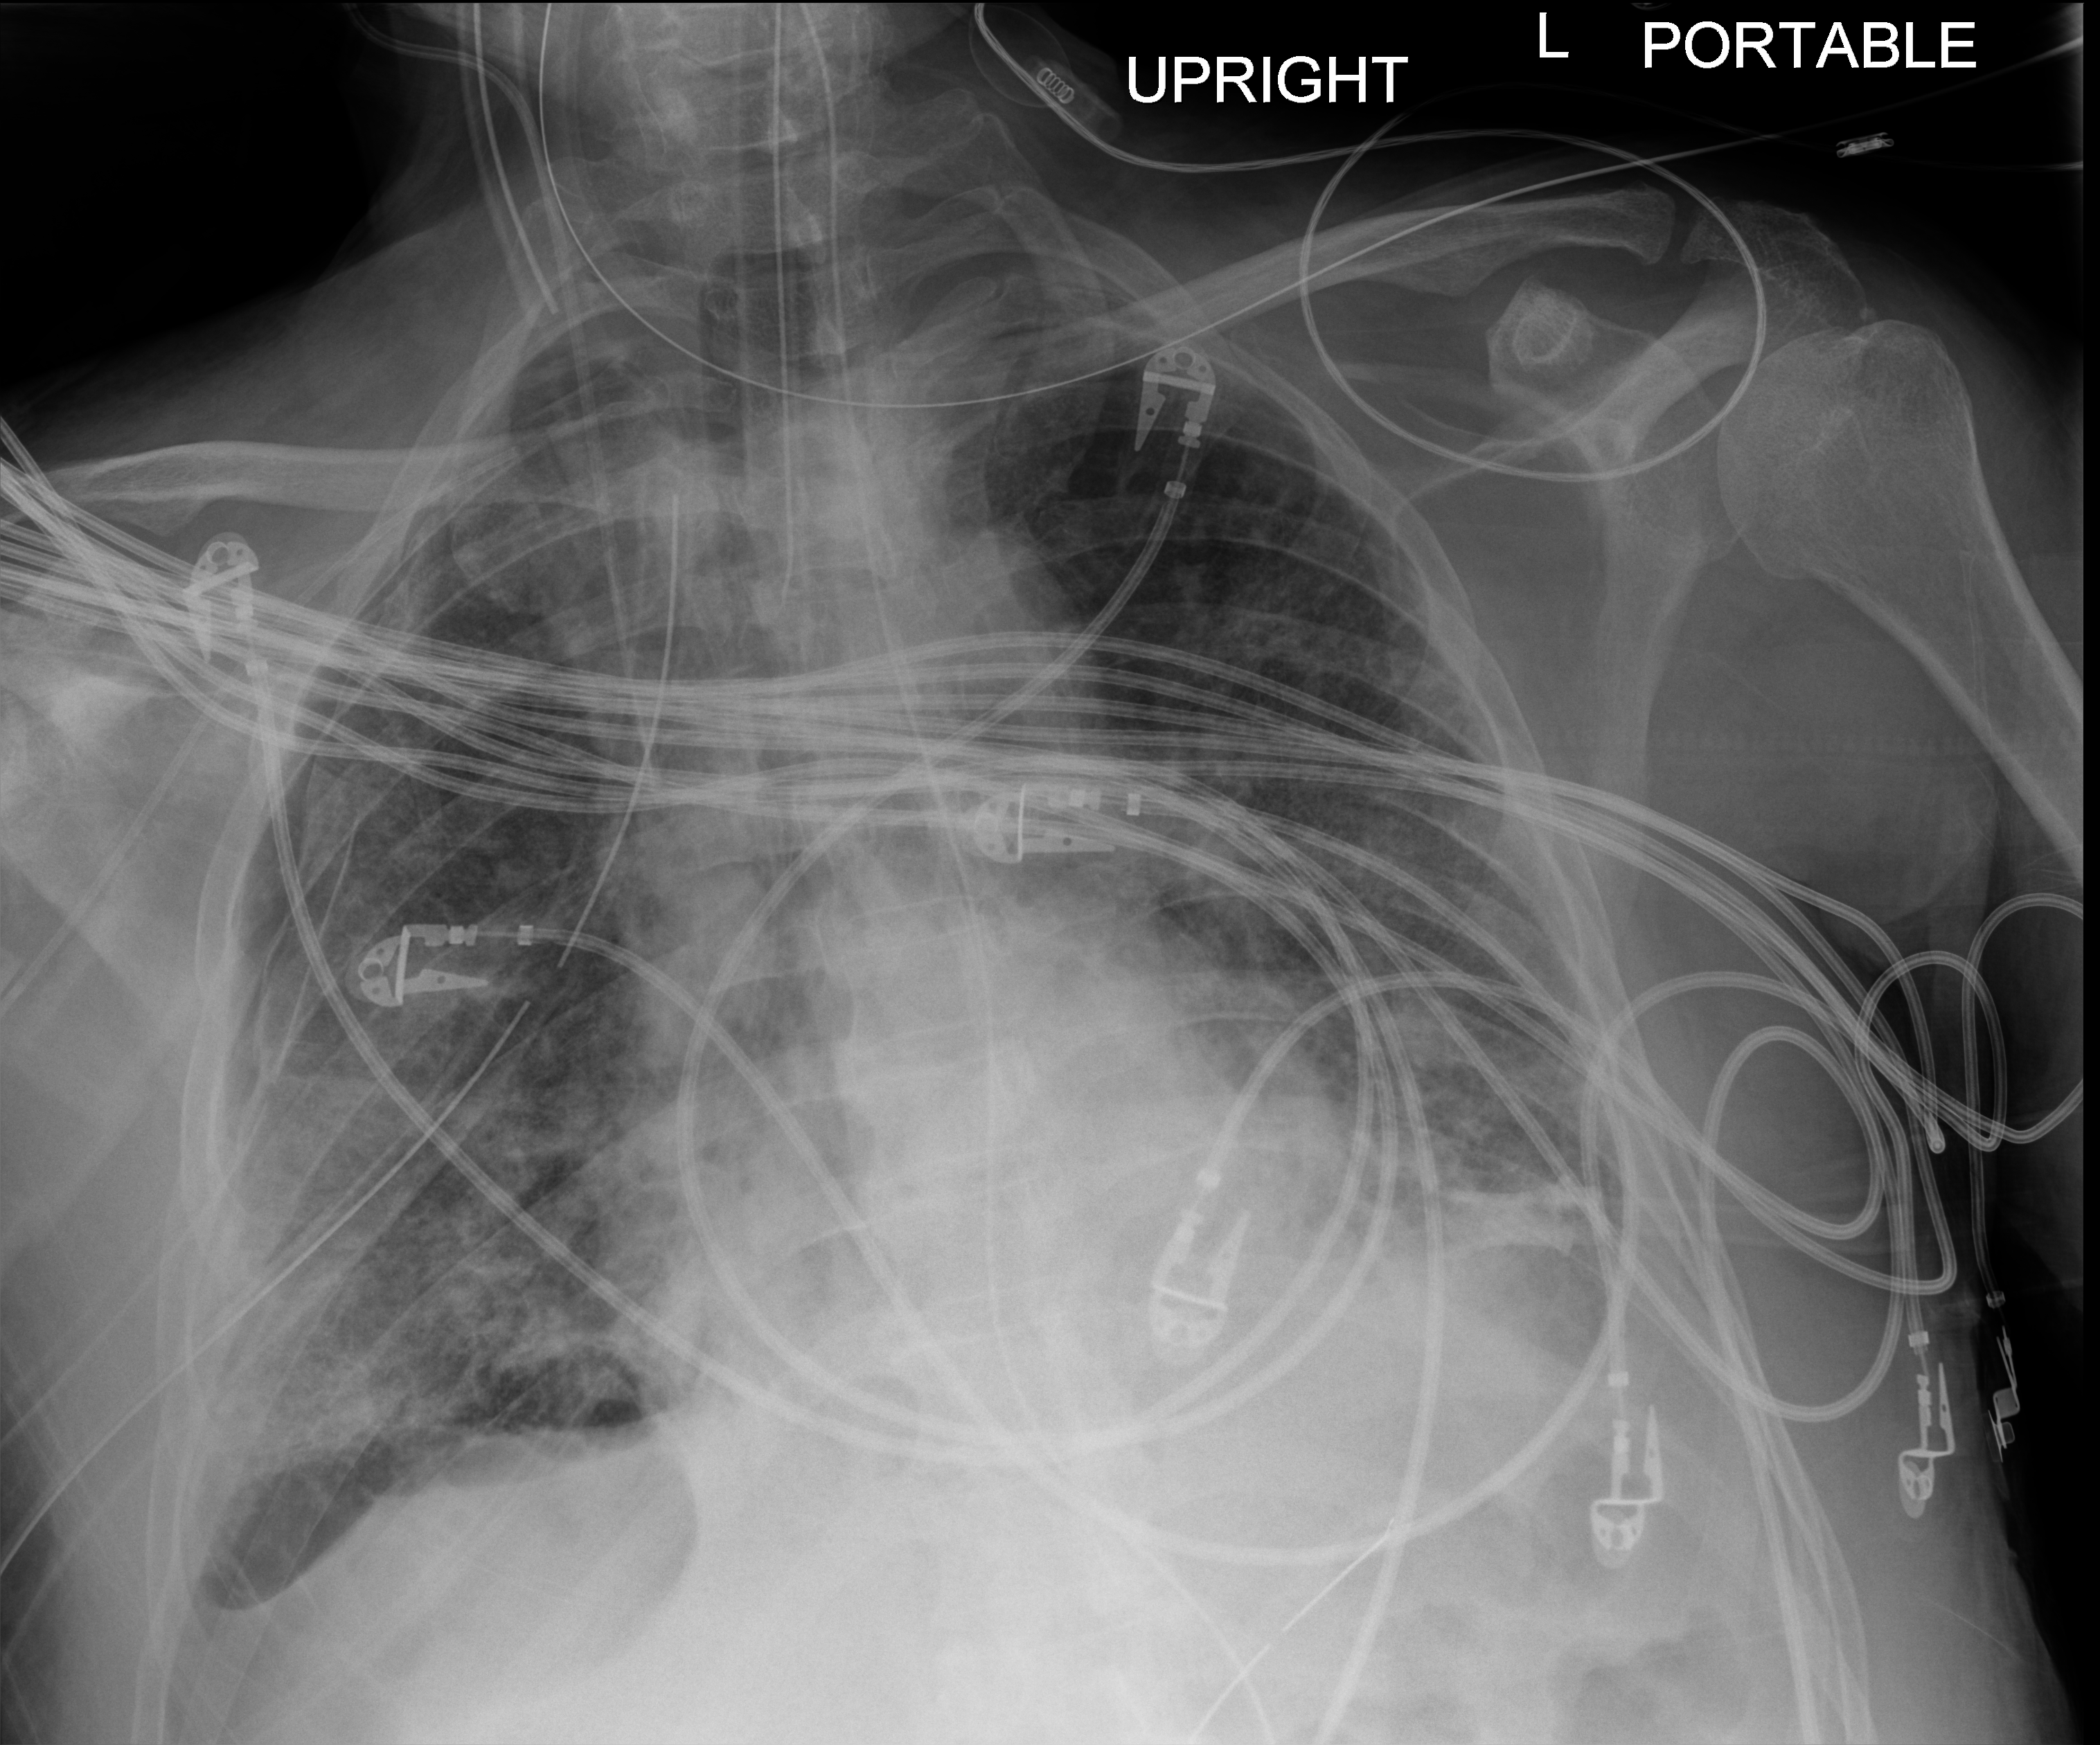
Chest X-ray (portable), anteroposterior (AP) projection. Patient hospitalised with COVID-19; male, aged 60–74 years.
Admission-level facts for this patient (not findings on this image; timing relative to this image not recorded):
- COPD (admission record): no
- length of hospital stay: 37 days